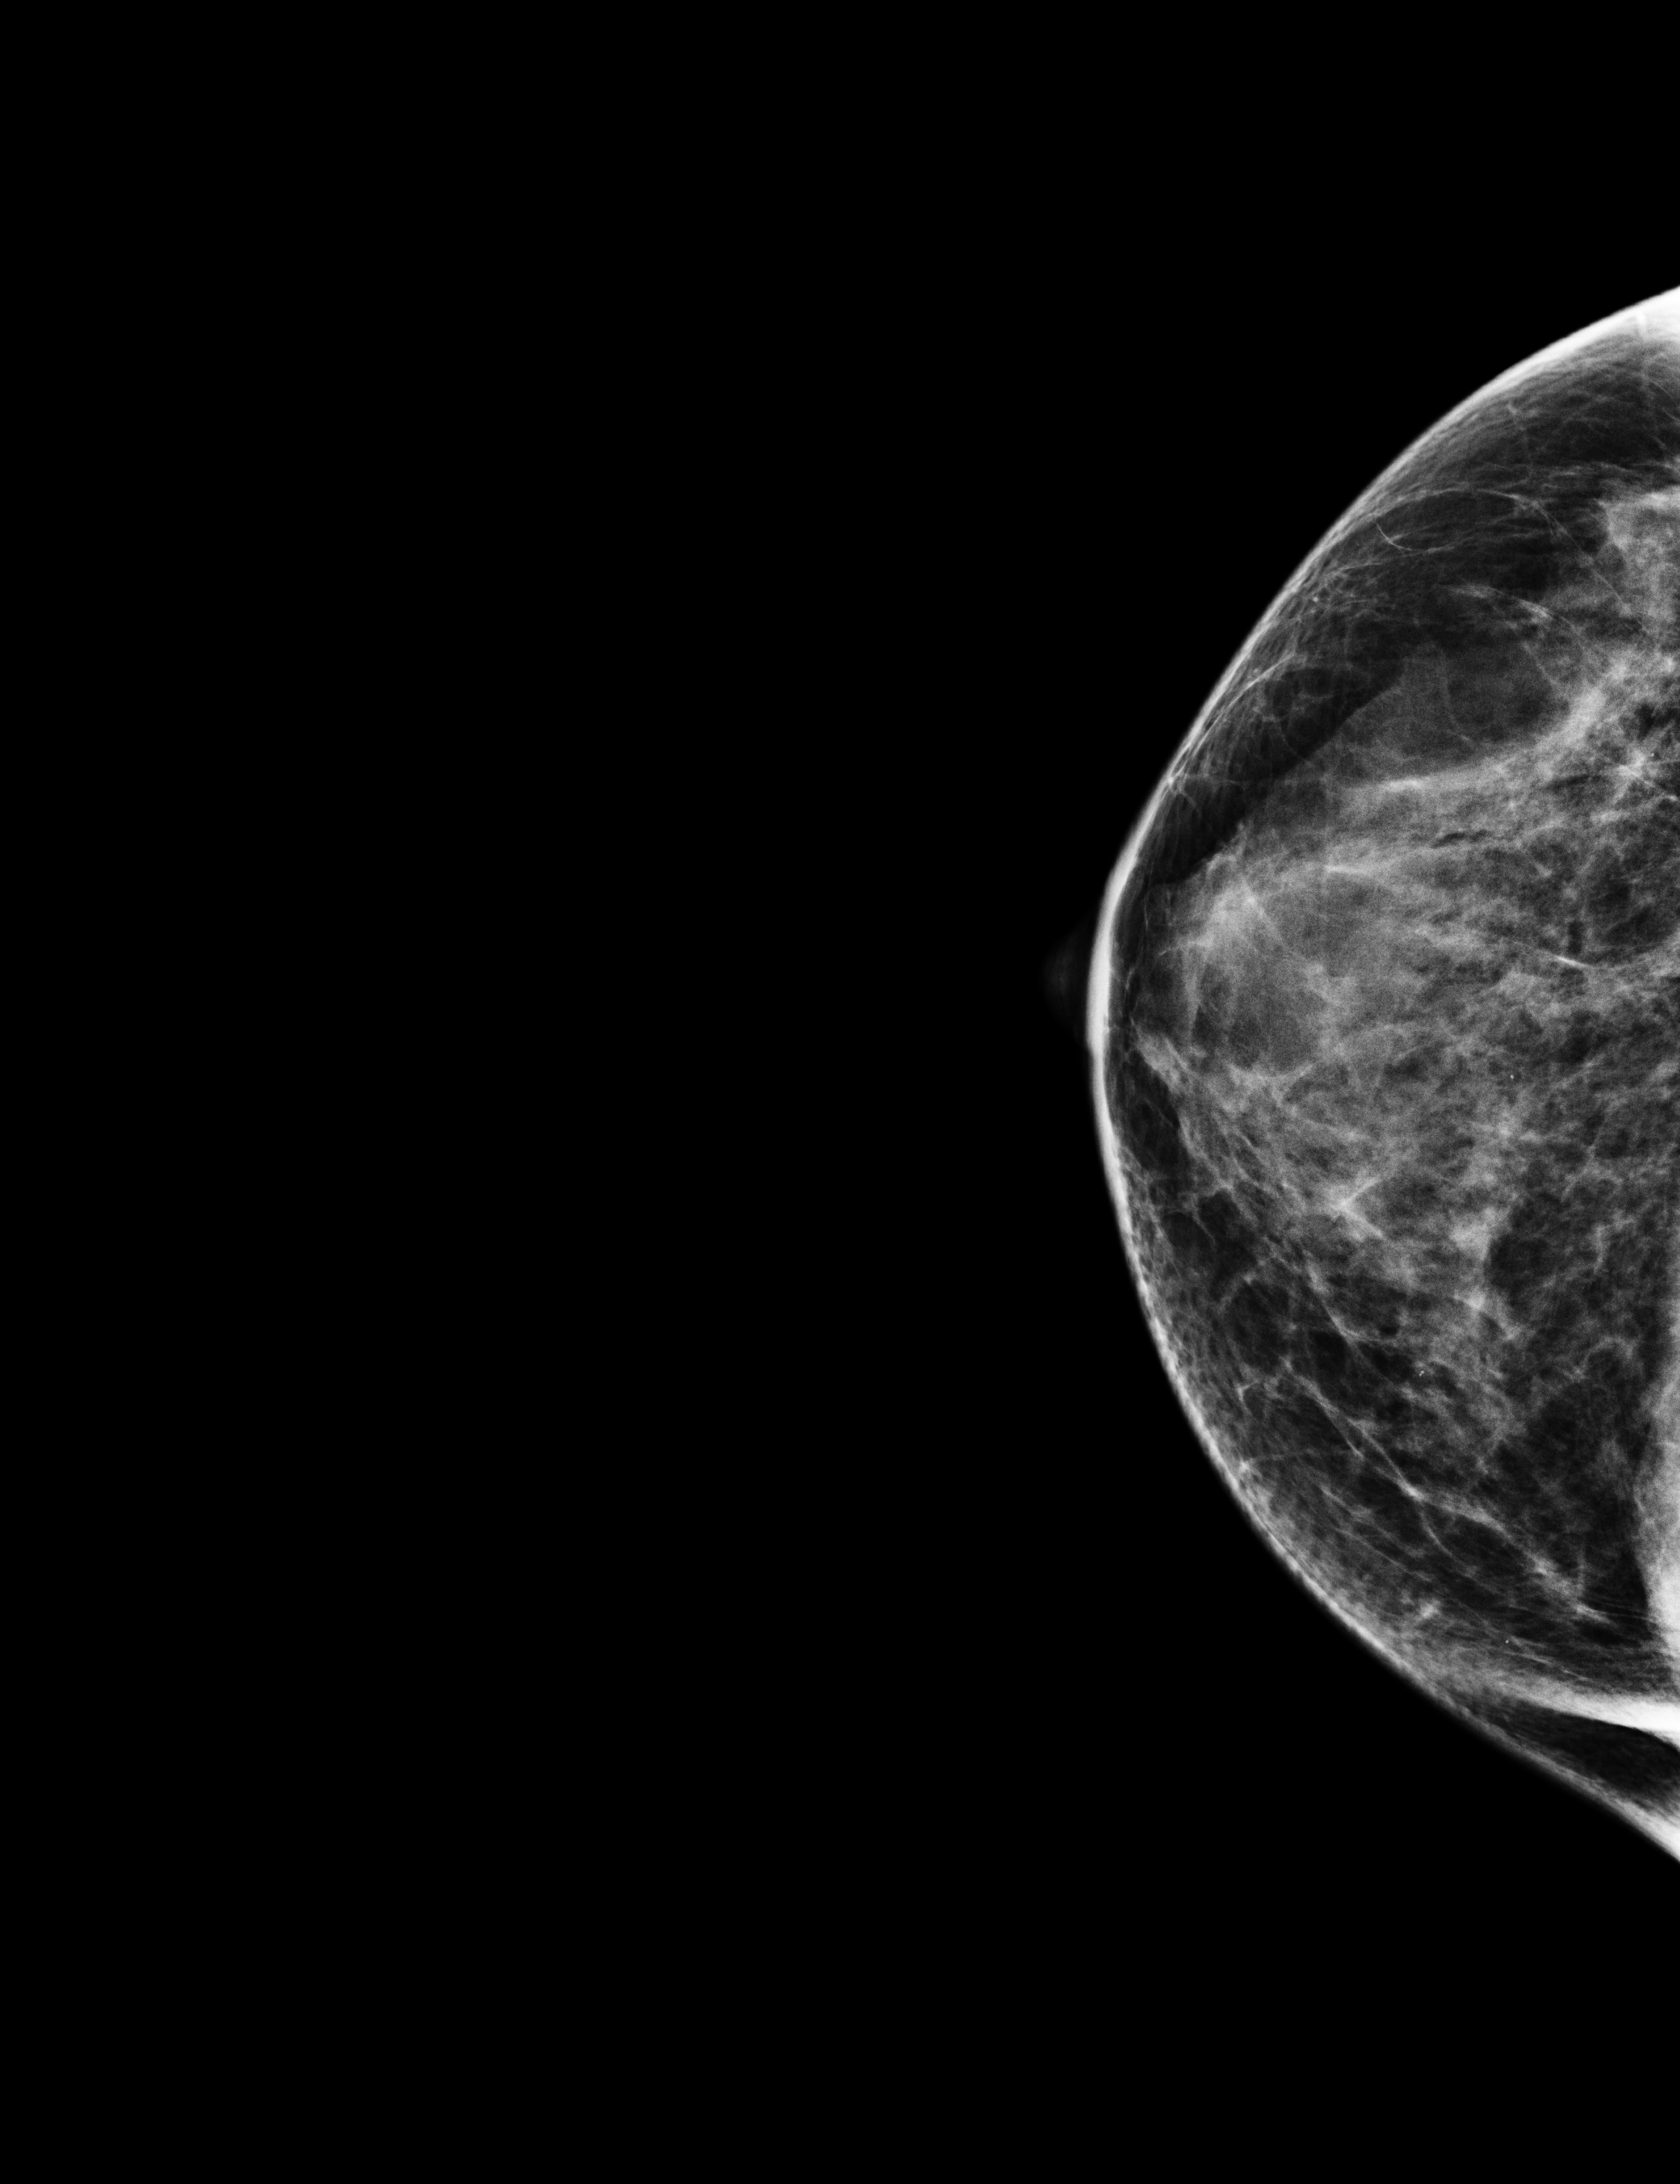
Screening examination; compressed breast thickness 58 mm; system: Selenia Dimensions. Patient: female, 56 years.
Image type: full-field digital mammogram. Breast: right. Projection: craniocaudal (CC) view.